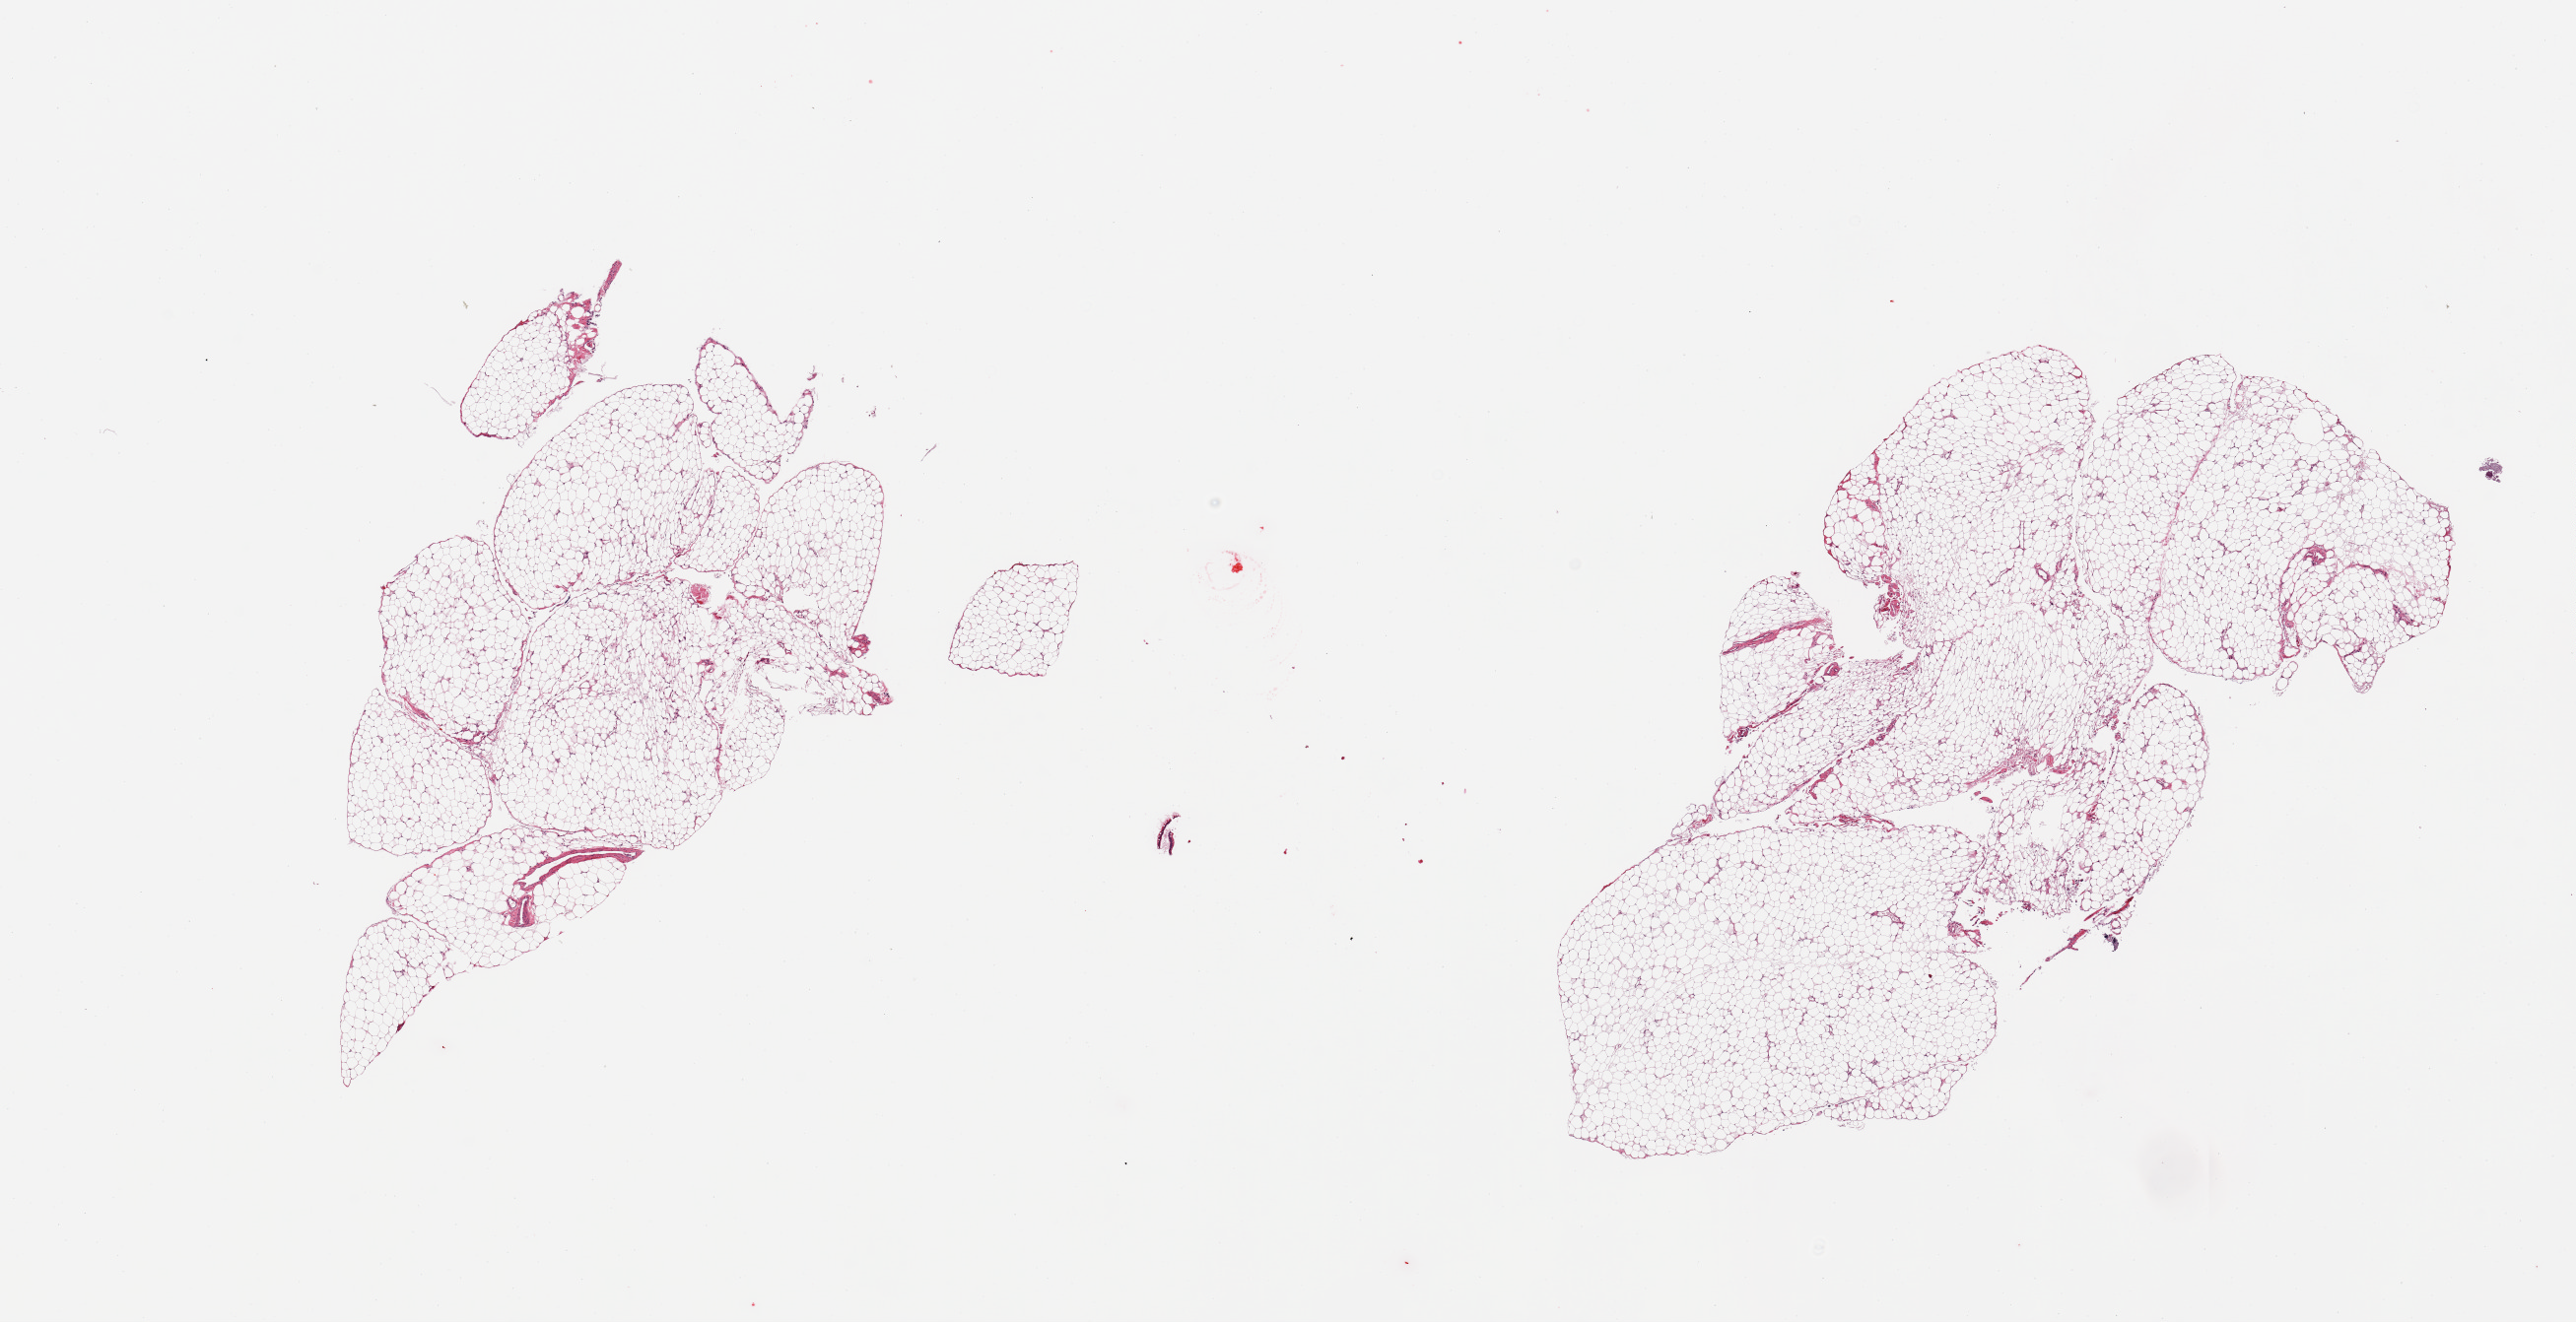
H&E whole-slide image, low-resolution overview of the scanned area, about 20.7 x 10.6 mm (from a 20x scan). PAXgene-fixed paraffin-embedded (PFPE) section. Sampled site (target tissue): omentum. Donor tissue sample. Donor: male.
Review note (as recorded): 2 pieces, no abnormalities.